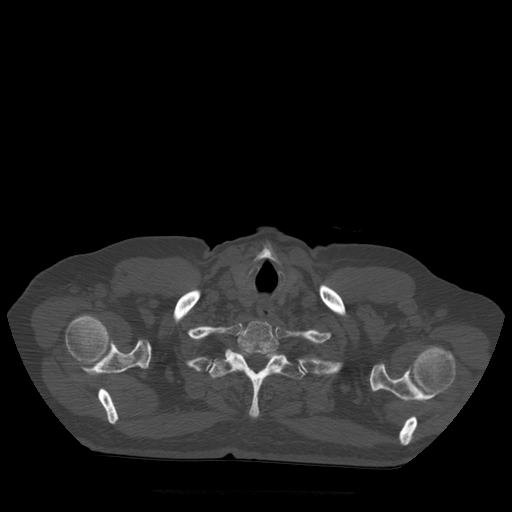
CT including the spine, one axial slice; position 432 of 522 along the scan axis; bone window (W 1800 / L 400 HU); 1.25 mm slice thickness; 512 × 512 image matrix, field of view 420 × 420 mm. Patient age 72 years. From the clinical record (not read from this slice): primary cancer: prostate.
Structures marked on this image (semi-automatically segmented with operator editing):
- T1 vertebra: box from (x=238, y=321) to (x=280, y=354) px
- T2 vertebra: (x=209, y=350)–(x=305, y=418)